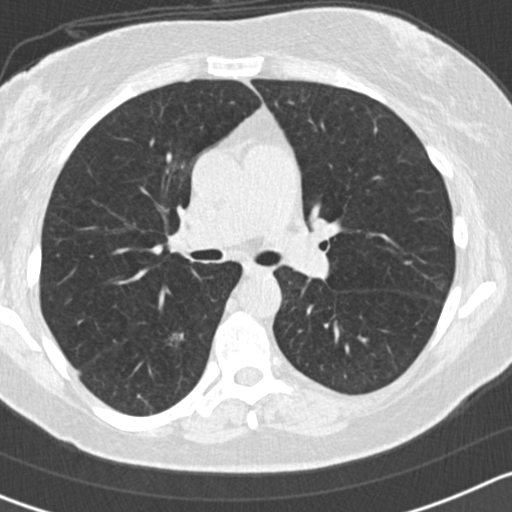
Low-dose screening chest CT, axial slice. First (baseline) screen. Lung window (W 1500 / L -600 HU). Slice 65 of 161 in the series. 512 × 512 image matrix, field of view 306 × 306 mm. Female, age 65 years at enrolment. Former smoker at enrolment.
Expert reader's lesion annotation, bounding box (x1, y1, x2, y2) in pixels: (145, 316, 200, 365). Reader record for this screening exam (exam-level; its link to the box is not recorded): non-calcified nodule or mass ≥4 mm, right lower lobe, 14 × 13 mm, spiculated (stellate) margins, mixed attenuation. Participant outcome: lung cancer diagnosed 565 days after this screen — adenocarcinoma, NOS, right lower lobe, moderately differentiated (G2), stage IA (AJCC 6th edition), 25 mm at pathology.